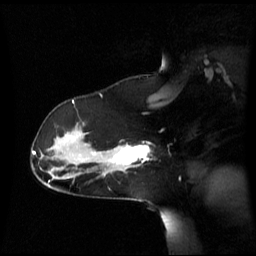
Breast MRI (dynamic contrast-enhanced), one sagittal slice. Position 41 of 60 along the scan axis. Dynamic contrast-enhanced series, image 2 of 3 at this slice position (ordered by acquisition). 1.5 T. TE 4.2 ms, TR 8.4 ms. 2.8 mm slice thickness. 256 × 256 image matrix, field of view 270 × 270 mm. Patient: female, 39 years. From the clinical record (not read from this slice): setting: breast cancer imaged before/during neoadjuvant chemotherapy; receptor status: triple-negative.
Annotated regions visible in this slice (semi-automatically segmented with operator editing):
- analysis volume of interest (the breast-tissue region the enhancement analysis was run in; not a lesion): box from (x=101, y=144) to (x=150, y=173) px
- tumour enhancement mask (voxels above the 70 % enhancement threshold inside the analysis volume of interest): (x=115, y=145)–(x=149, y=165)